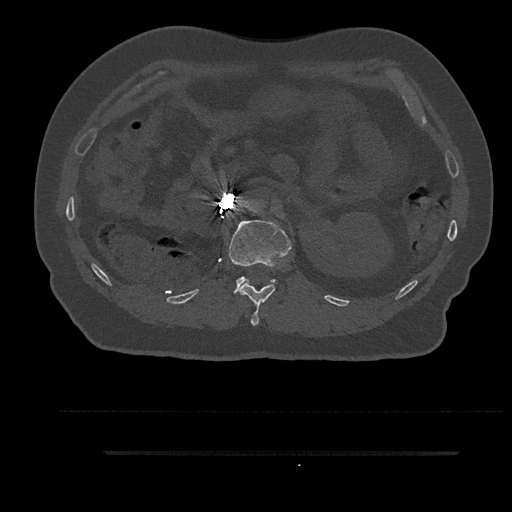
CT including the spine, one axial slice; position 206 of 797 along the scan axis; reconstruction kernel Br40s/3; bone window (W 1800 / L 400 HU); 512 × 512 image matrix. Male patient, age 63 years. From the clinical record (not read from this slice): primary cancer: renal; vertebrae with lytic lesions (as recorded): T8.
Structures marked on this image (semi-automatically segmented with operator editing):
- L1 vertebra: box from (x=228, y=220) to (x=291, y=294) px
- T12 vertebra: (x=239, y=281)–(x=275, y=326)